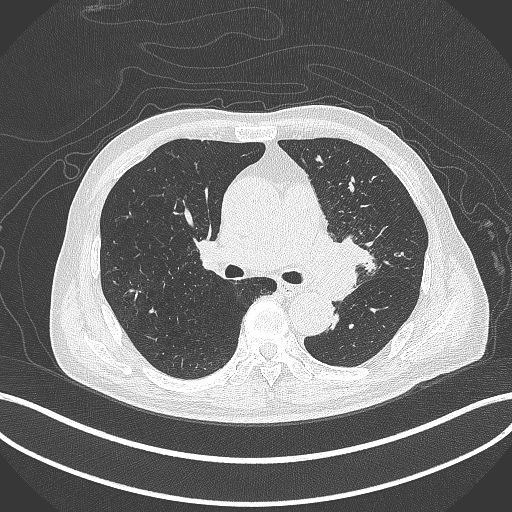
Chest CT, one axial slice. Slice 258 of 417 in the series (ordered by position). 120 kVp. Lung window (W 1500 / L -600 HU). 1 mm slice thickness. 512 × 512 image matrix, field of view 400 × 400 mm. Patient: male, 77 years. Case-level facts recorded for this patient, not image findings: clinical TNM (as recorded): T3 N1 M0.
Outlined on this slice (rectangle marked by the reading radiologist):
- lung tumour (recorded histology: adenocarcinoma): bounding box [x1, y1, x2, y2] px = [309, 228, 374, 304]